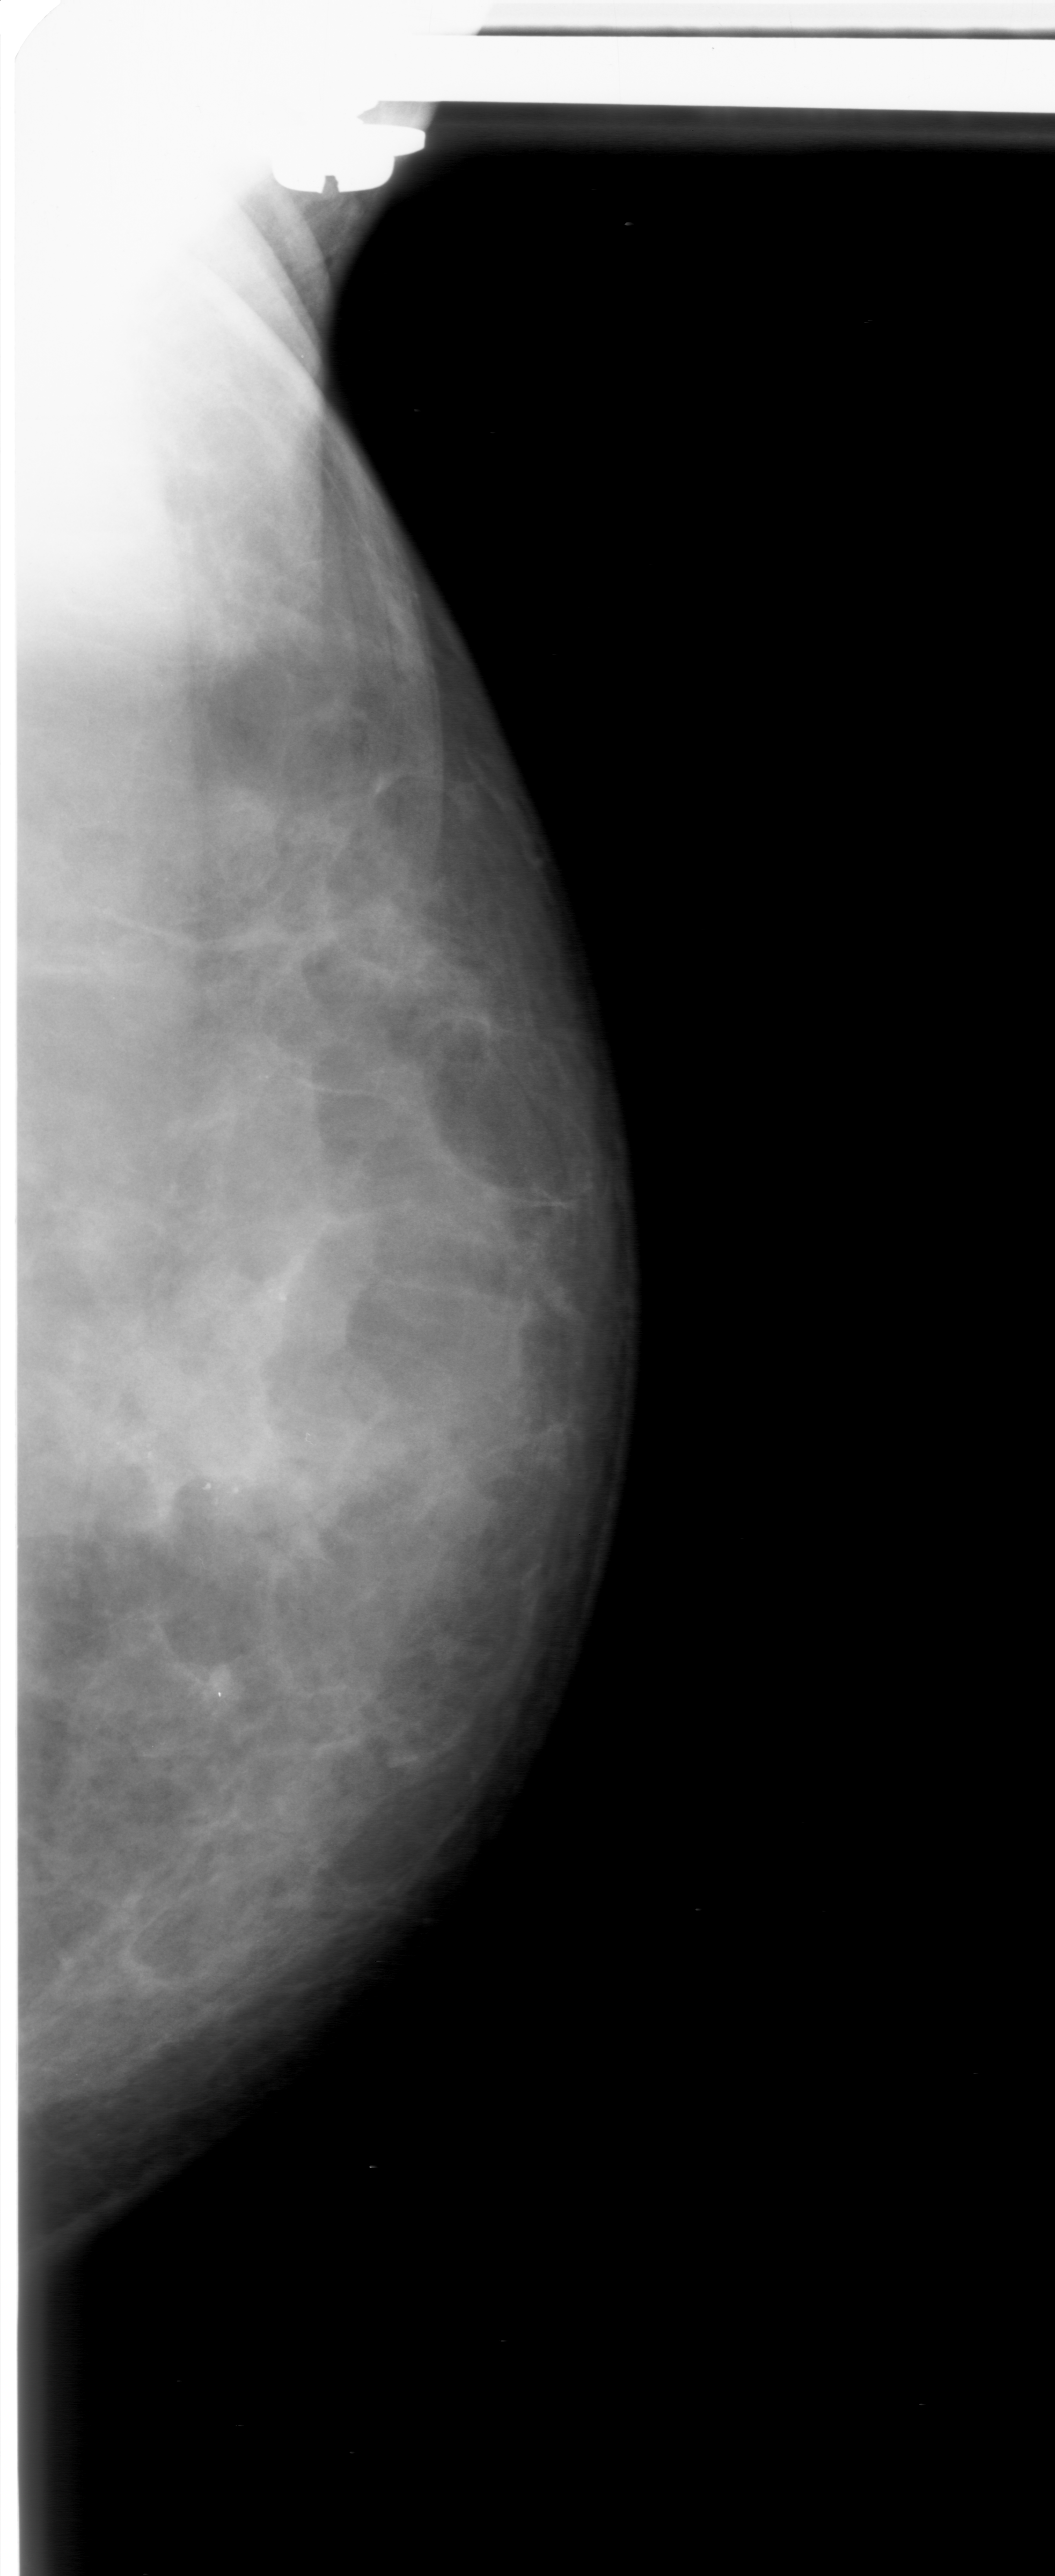
Digitized screen-film mammogram. Left breast. Craniocaudal (CC) view. BI-RADS breast density category 3 (scale 1–4). 1055 × 2576 image matrix.
Expert-marked regions of interest on this film, with their recorded descriptors:
- calcifications, morphology round and regular / pleomorphic, distribution clustered; BI-RADS assessment category 0 (incomplete: needs additional imaging); pathology (as recorded): benign: bounding box <63,1348,410,1543> (left, top, right, bottom; pixels)